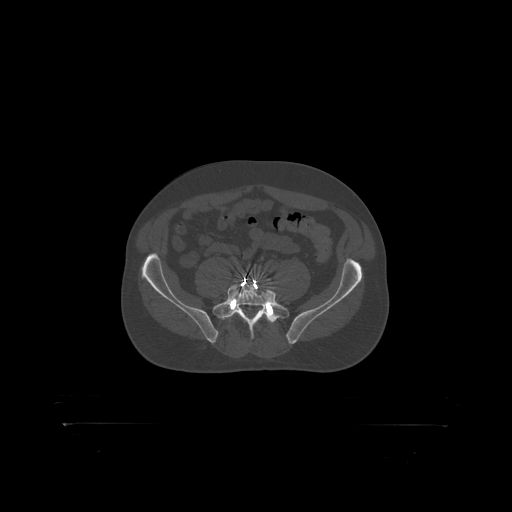
CT including the spine, one axial slice. Slice 188 of 399 in the series (ordered by position). Bone window (W 1800 / L 400 HU). 512 × 512 image matrix, field of view 650 × 650 mm. Male patient, age 46 years. From the clinical record (not read from this slice): primary cancer: skin.
Outlined on this slice (semi-automatic segmentation, software-assisted and operator-edited):
- L5 vertebra: box from (x=265, y=280) to (x=268, y=282) px